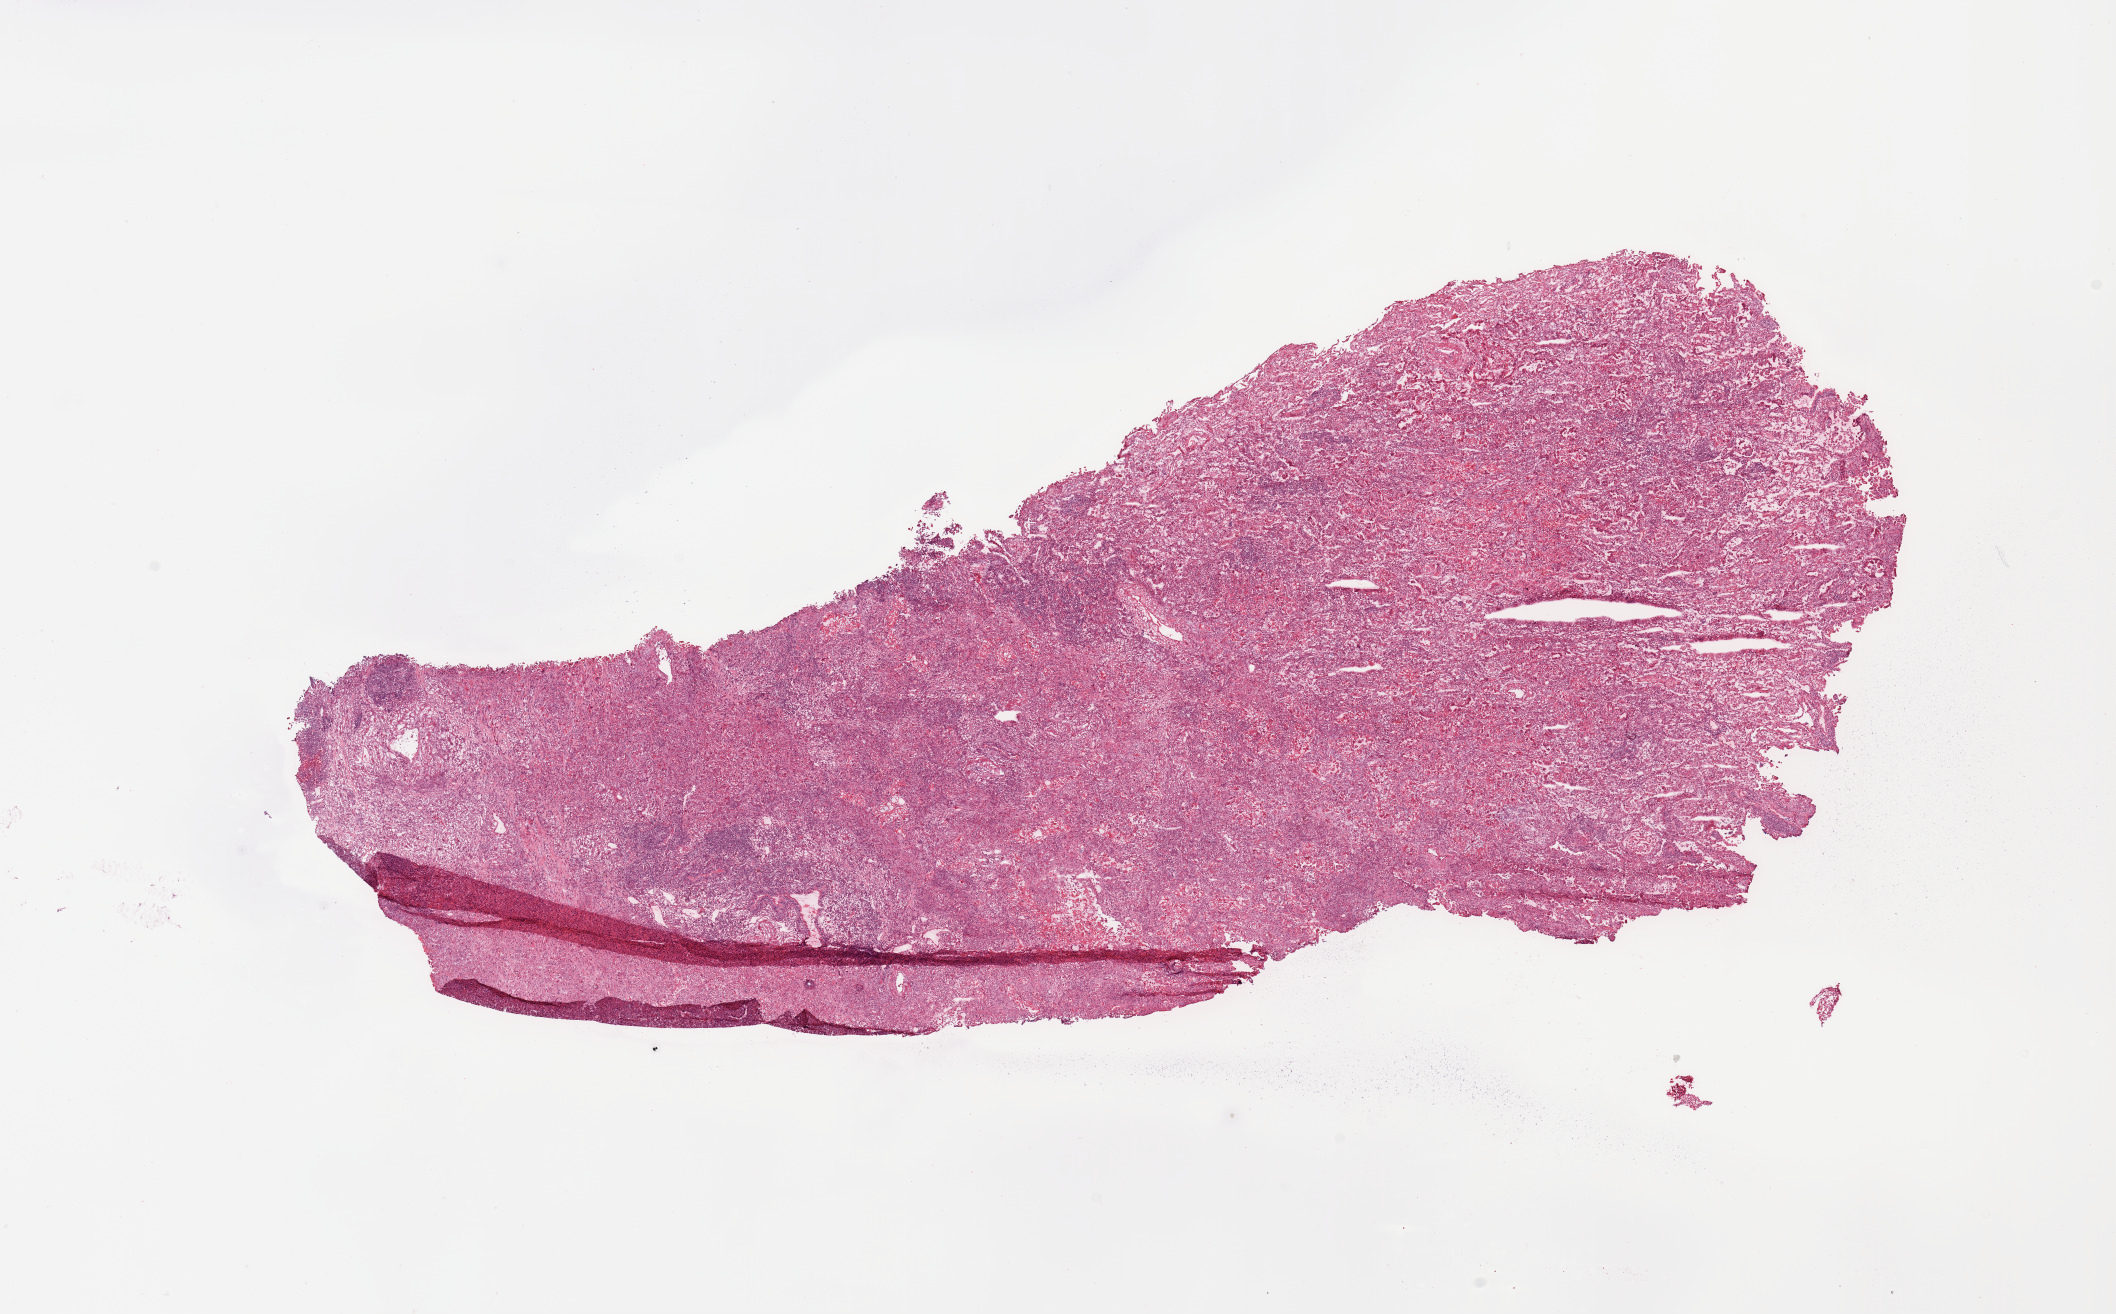
Whole-slide histology image, H&E — low-resolution overview of the scanned area, about 16.7 x 10.4 mm (slide scanned at 20x). Tumour tissue sample, sampled site: lung. Male, 79 y/o. Slide review estimates, as recorded: tumour nuclei 80%, necrosis 5%.
Histologic diagnosis: Adenocarcinoma, NOS.